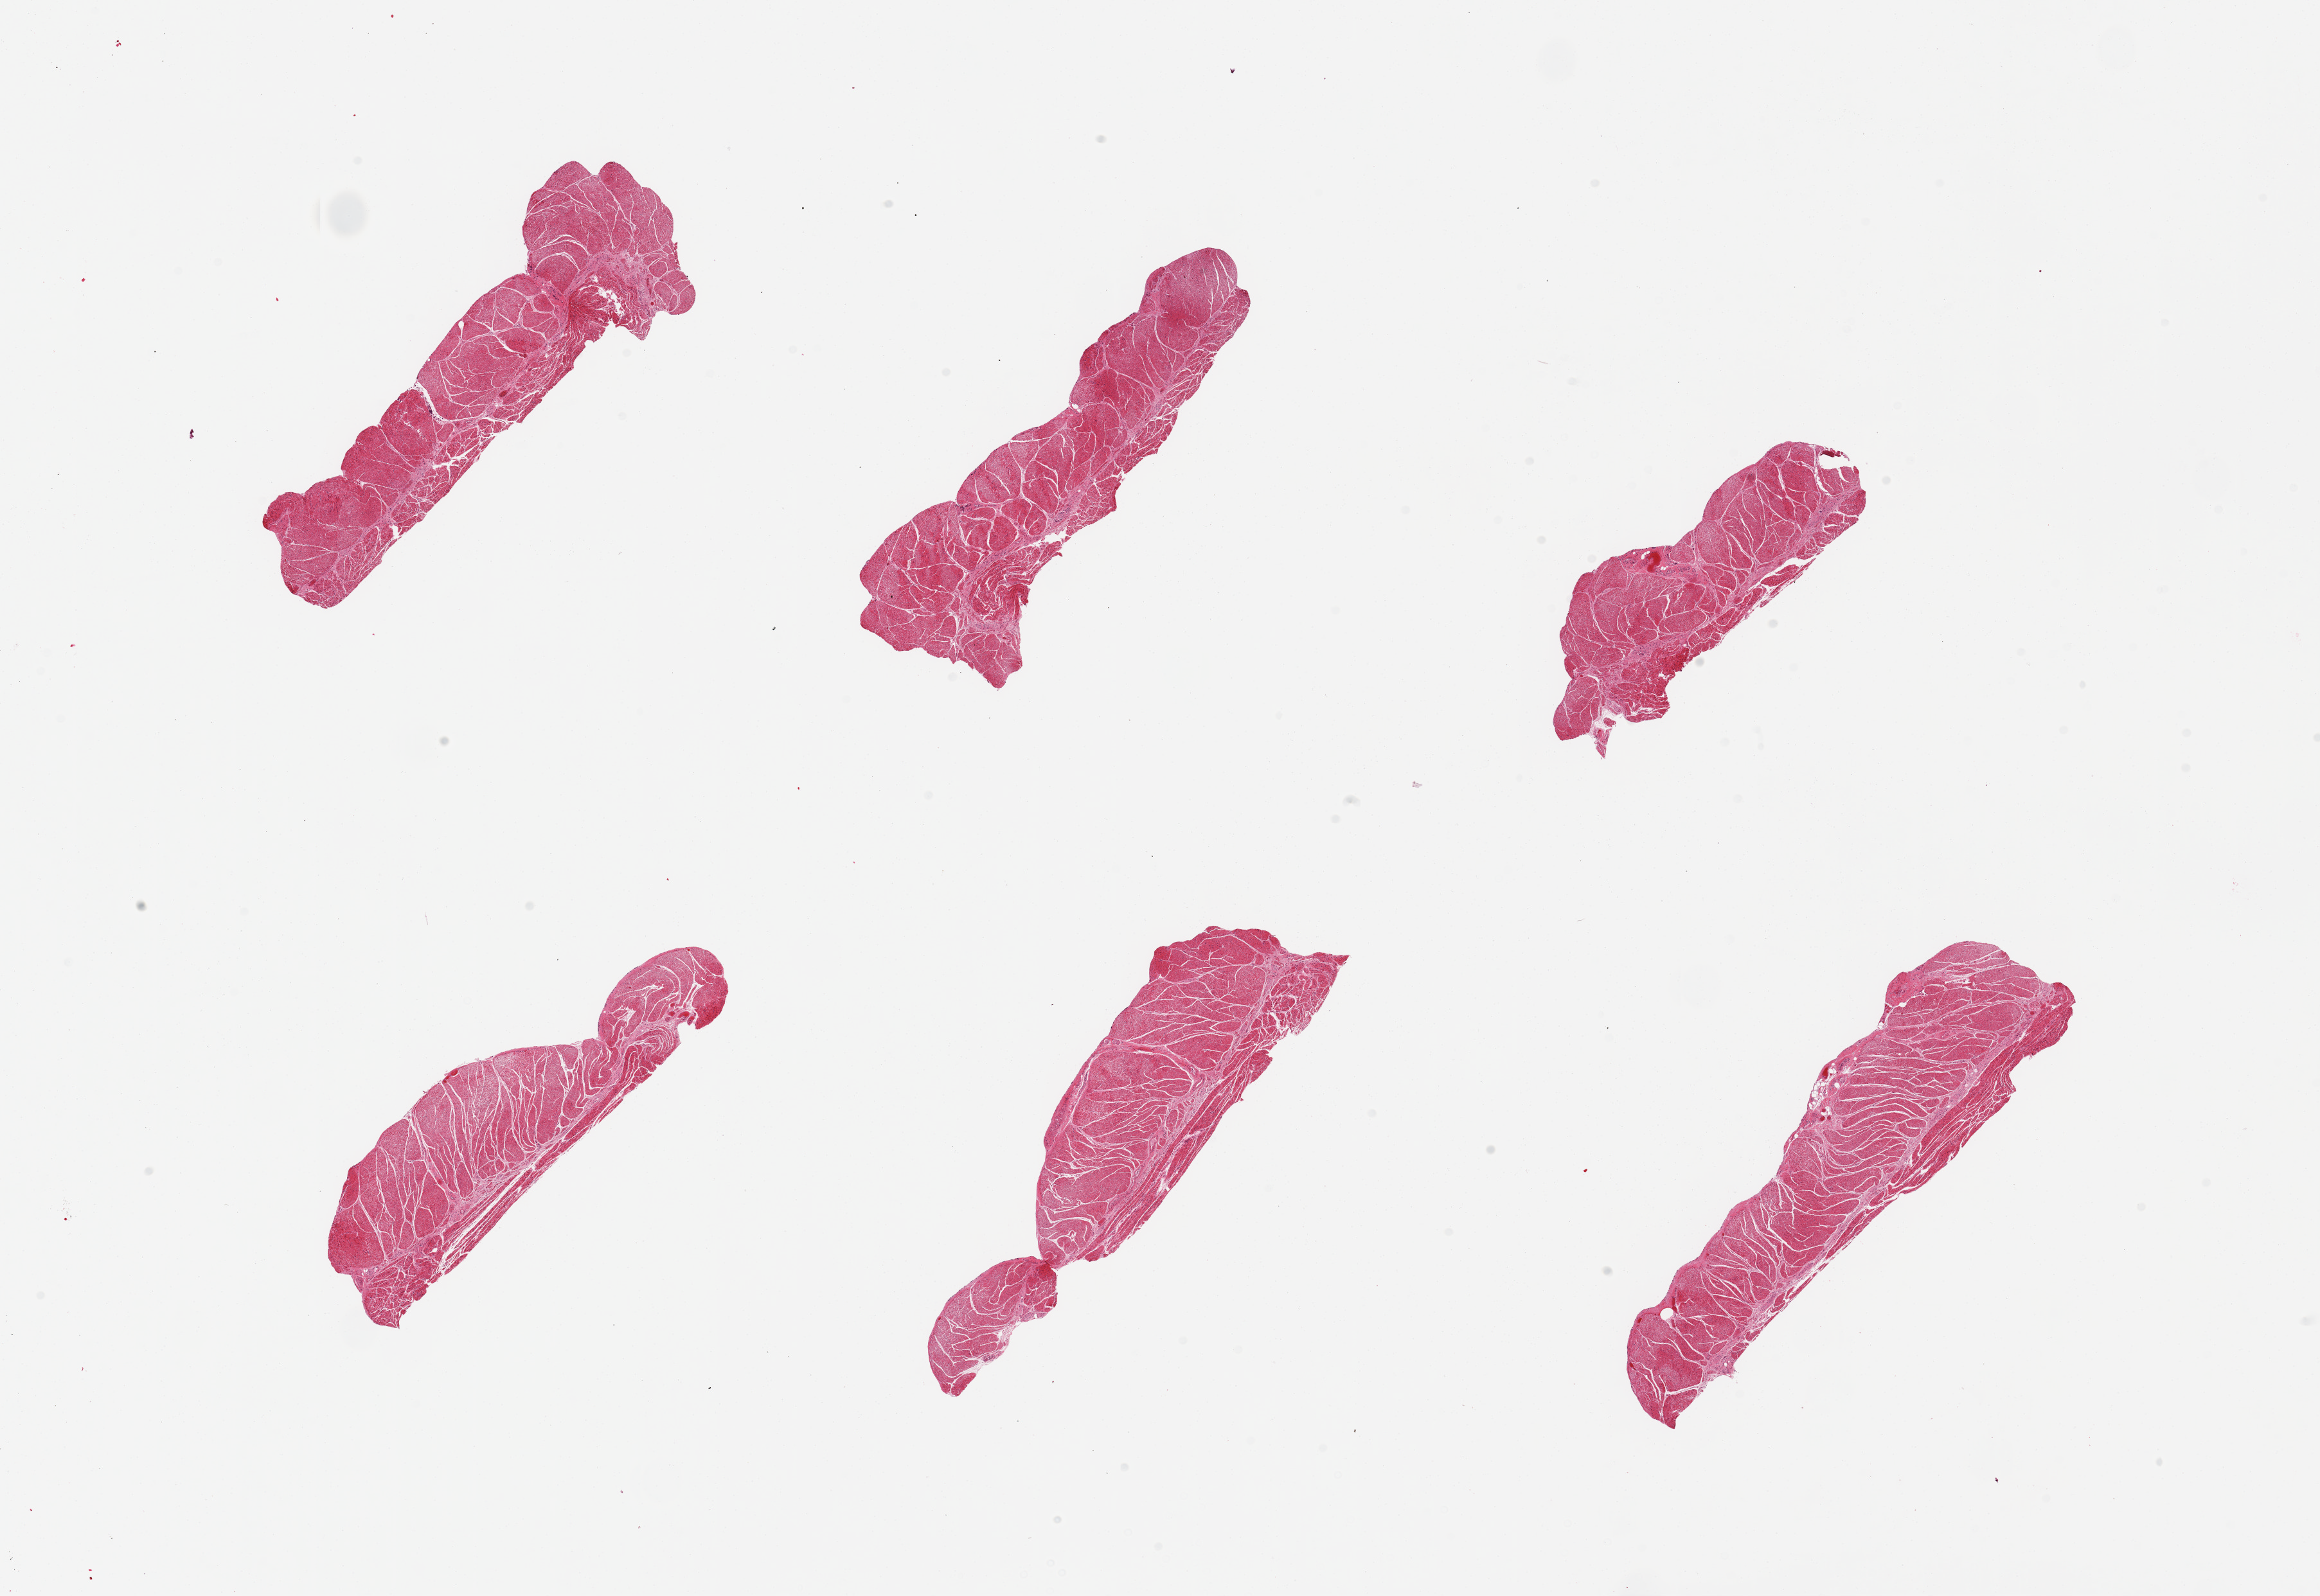
Whole-slide image, H&E stain, brightfield, low-resolution overview of the scanned area, about 28.5 x 19.6 mm; PAXgene-fixed, paraffin-embedded tissue; target tissue: gastroesophageal junction; tissue donor sample. Male donor.
Review note (as recorded): 6 pieces; well trimmed.